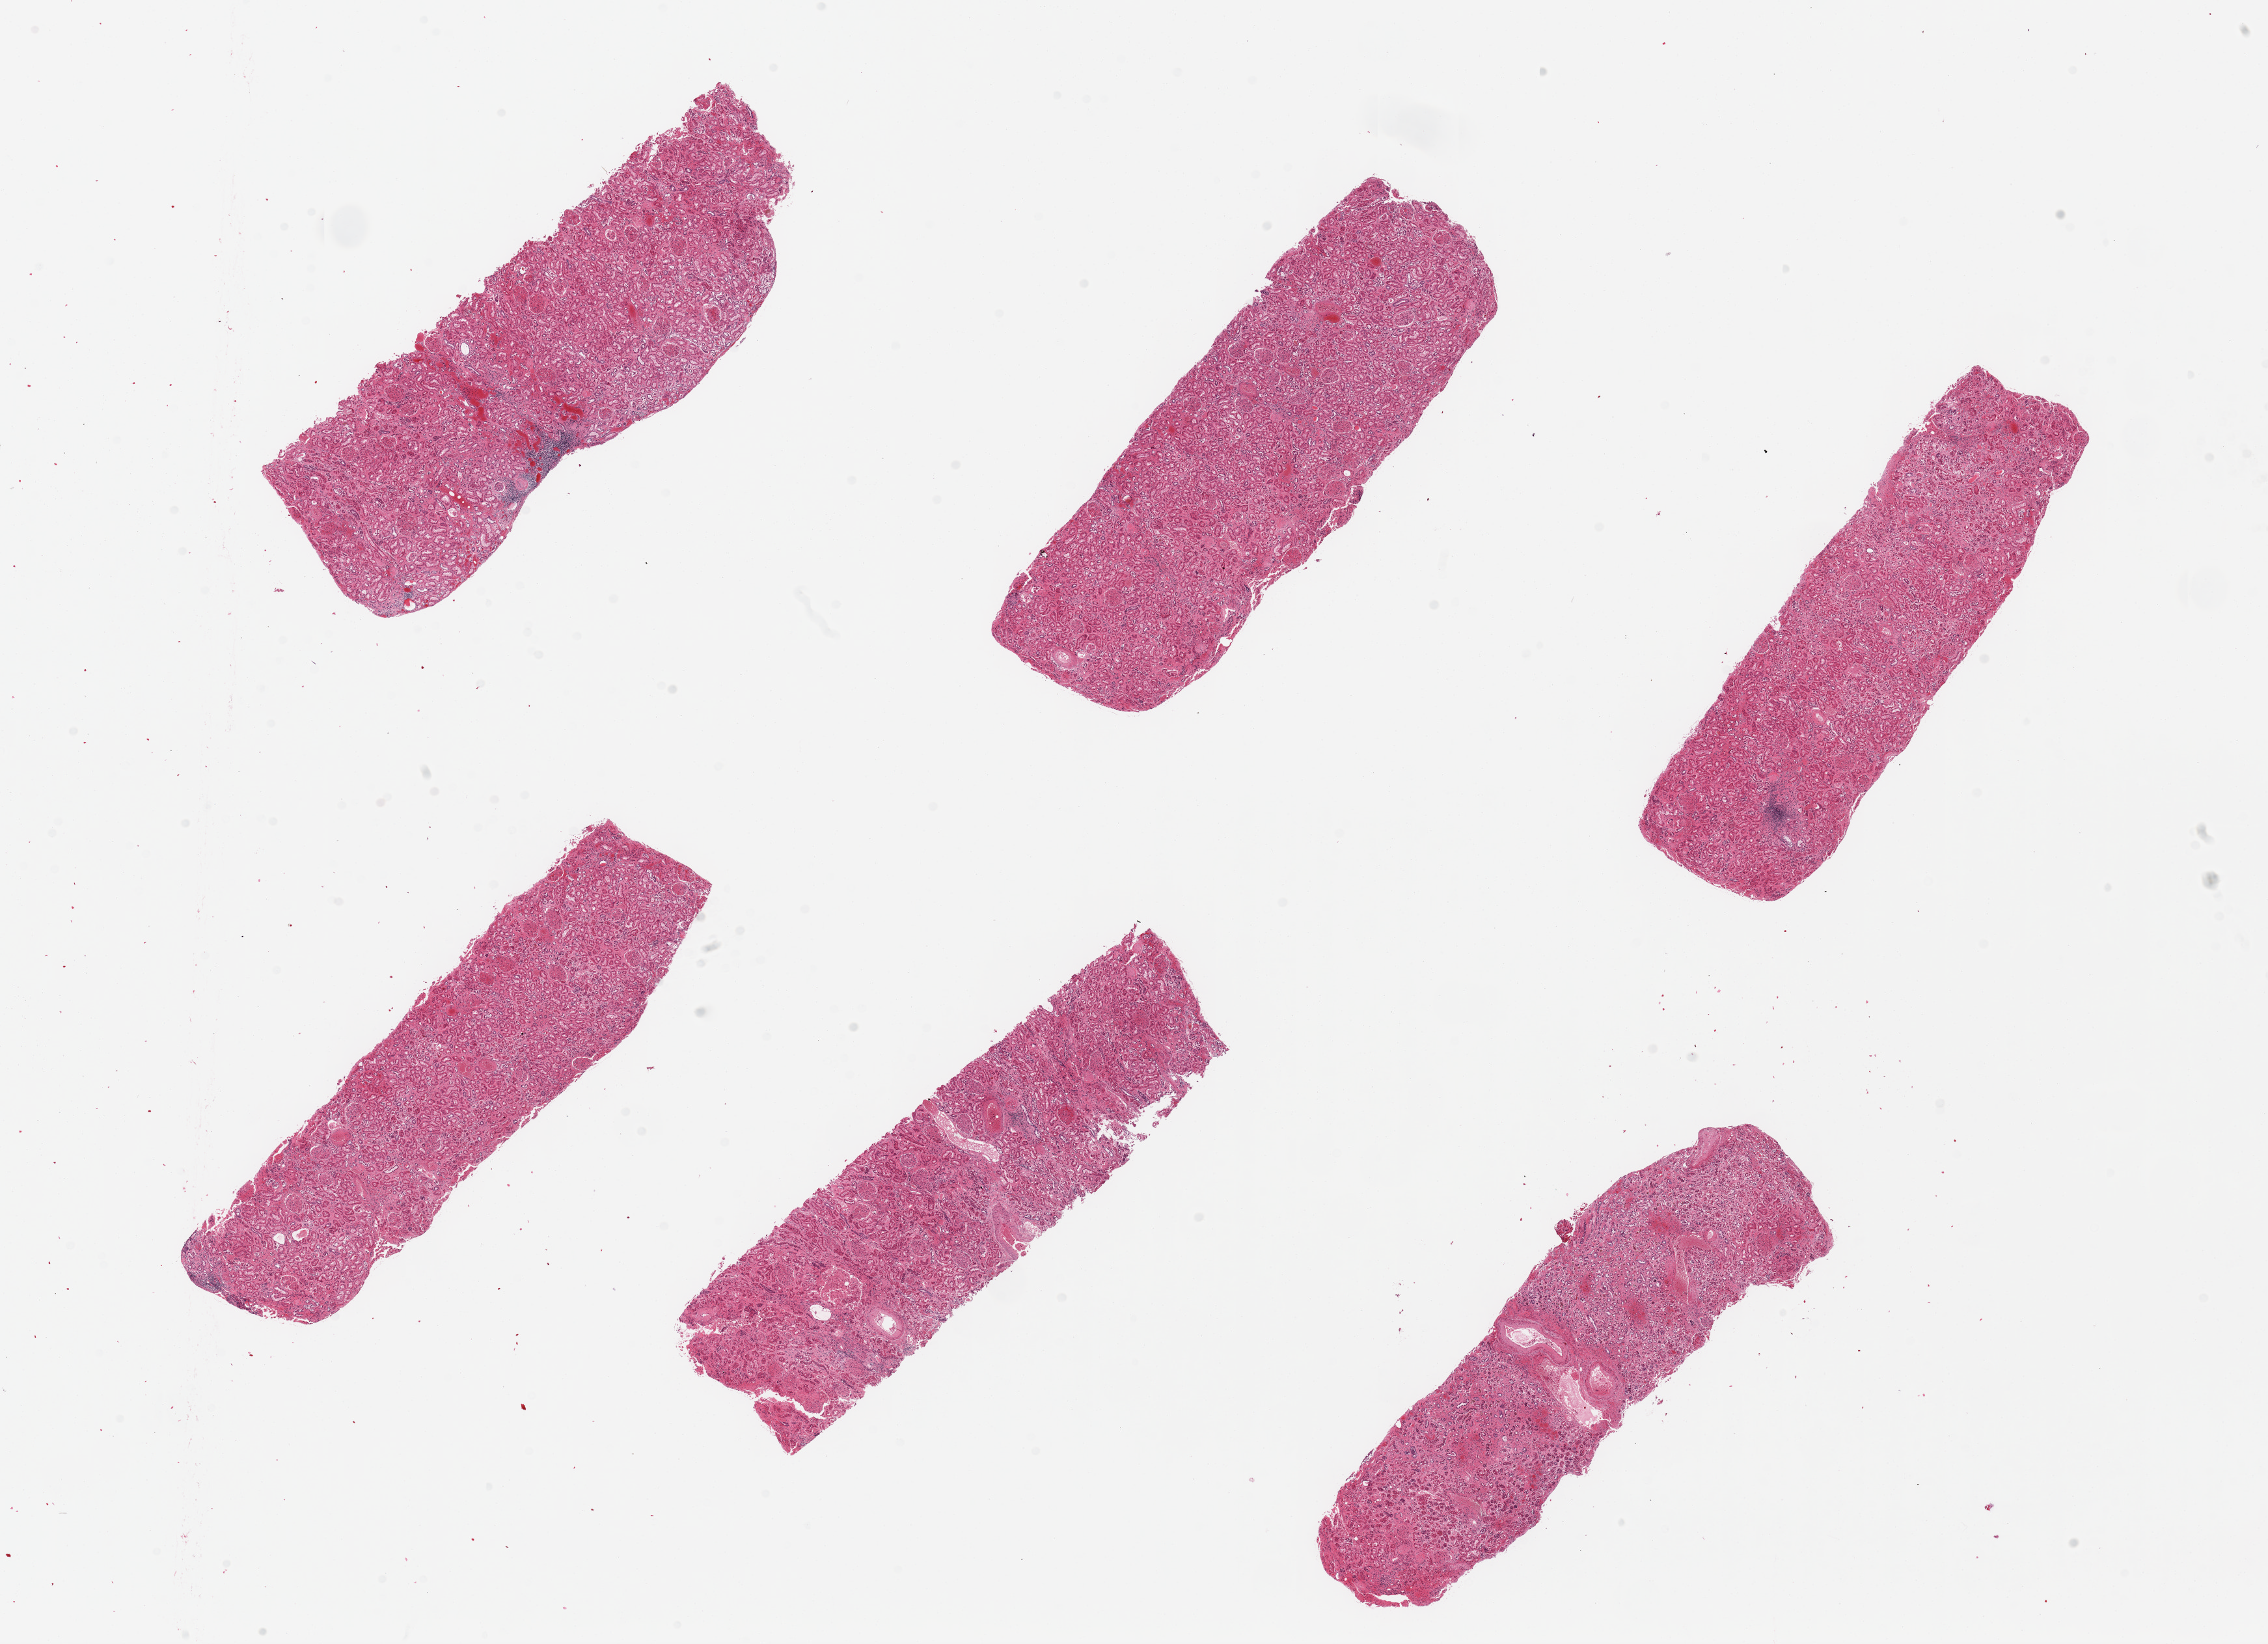
H&E whole-slide image — low-resolution overview of the scanned area, about 27.6 x 20.0 mm (slide scanned at 20x). PAXgene-fixed paraffin-embedded (PFPE) section. Target tissue: renal cortex. Donor tissue sample. Female donor.
Pathologist's review note for this sample: 6 pieces; congested, arterial sclerosis, occasional sclerosed glomeruli.